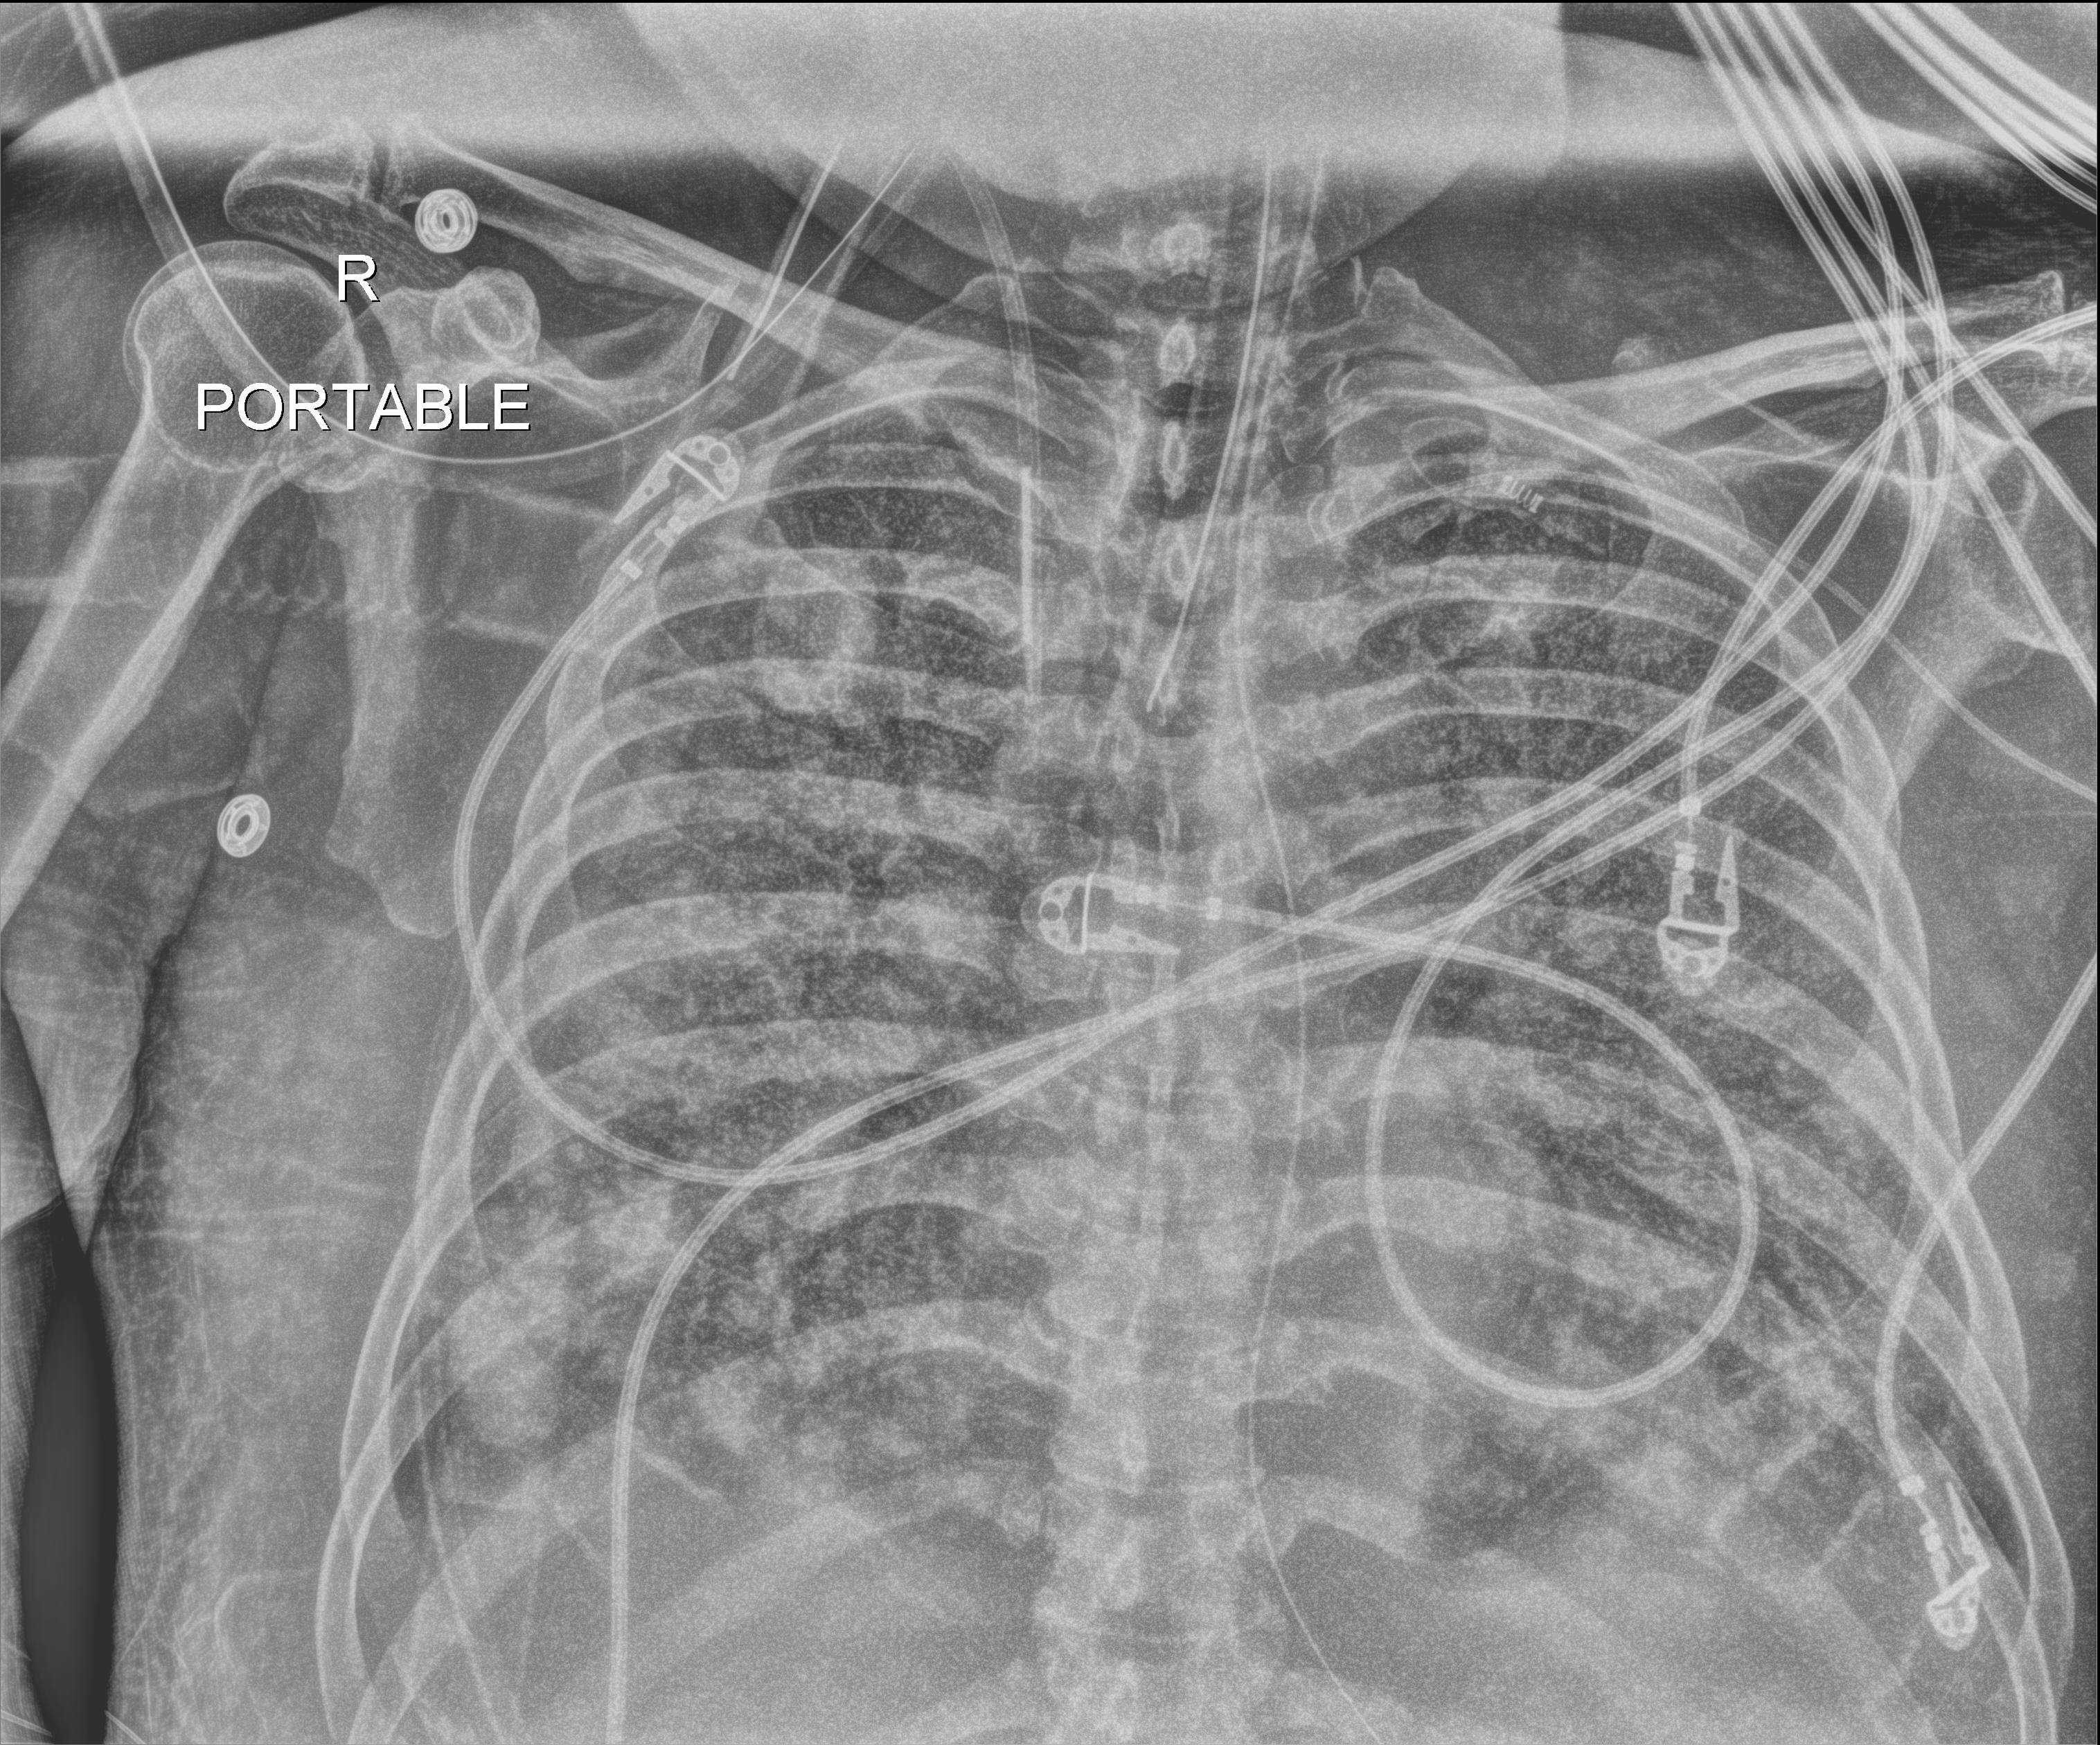
Portable chest radiograph. Male patient hospitalised with COVID-19, age 60–74 years.
Admission-level facts for this patient (not findings on this image; timing relative to this image not recorded):
- chronic kidney disease (admission record): no